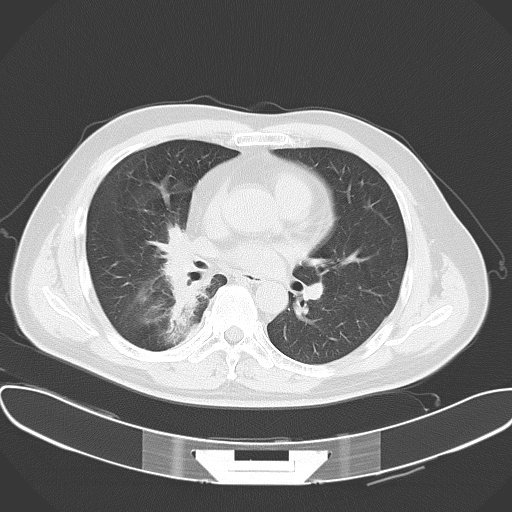
Chest CT, one axial slice; reconstruction kernel B70f; lung window (W 1500 / L -600 HU); 512 × 512 image matrix, field of view 388 × 388 mm. Patient: male, 48 years. Case-level facts recorded for this patient, not image findings: clinical TNM (as recorded): T1a N1 M1c; histopathological grade: G3.
Outlined on this slice (bounding box drawn by a radiologist):
- lung tumour (recorded histology: adenocarcinoma): box from (x=156, y=217) to (x=210, y=319) px